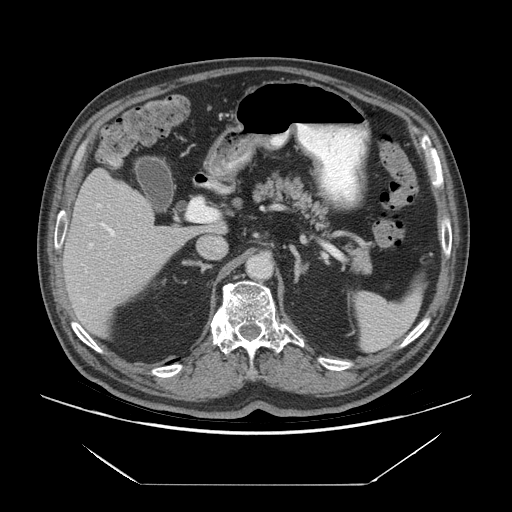
Contrast-enhanced abdominal CT (liver protocol), one axial slice. Slice 36 of 75 in the series (ordered by position). Soft-tissue window (W 400 / L 40 HU). 2.5 mm slice thickness. 512 × 512 image matrix. Case-level facts recorded for this patient, not image findings: diagnosis: hepatocellular carcinoma (patient treated with transarterial chemoembolisation; whether this scan precedes or follows treatment is not stated here); TNM stage (as recorded): Stage-I; Child-Pugh class: A; tumour differentiation: well differentiated; tumour size: 5.8 cm.
Annotated regions visible in this slice (semi-automatically segmented with operator editing):
- liver parenchyma outside the tumour (the mass and vessels are separate outlines, so this box may not span the whole liver): bounding box <62,168,196,336> (left, top, right, bottom; pixels)
- liver vessels: <81,203,115,302>